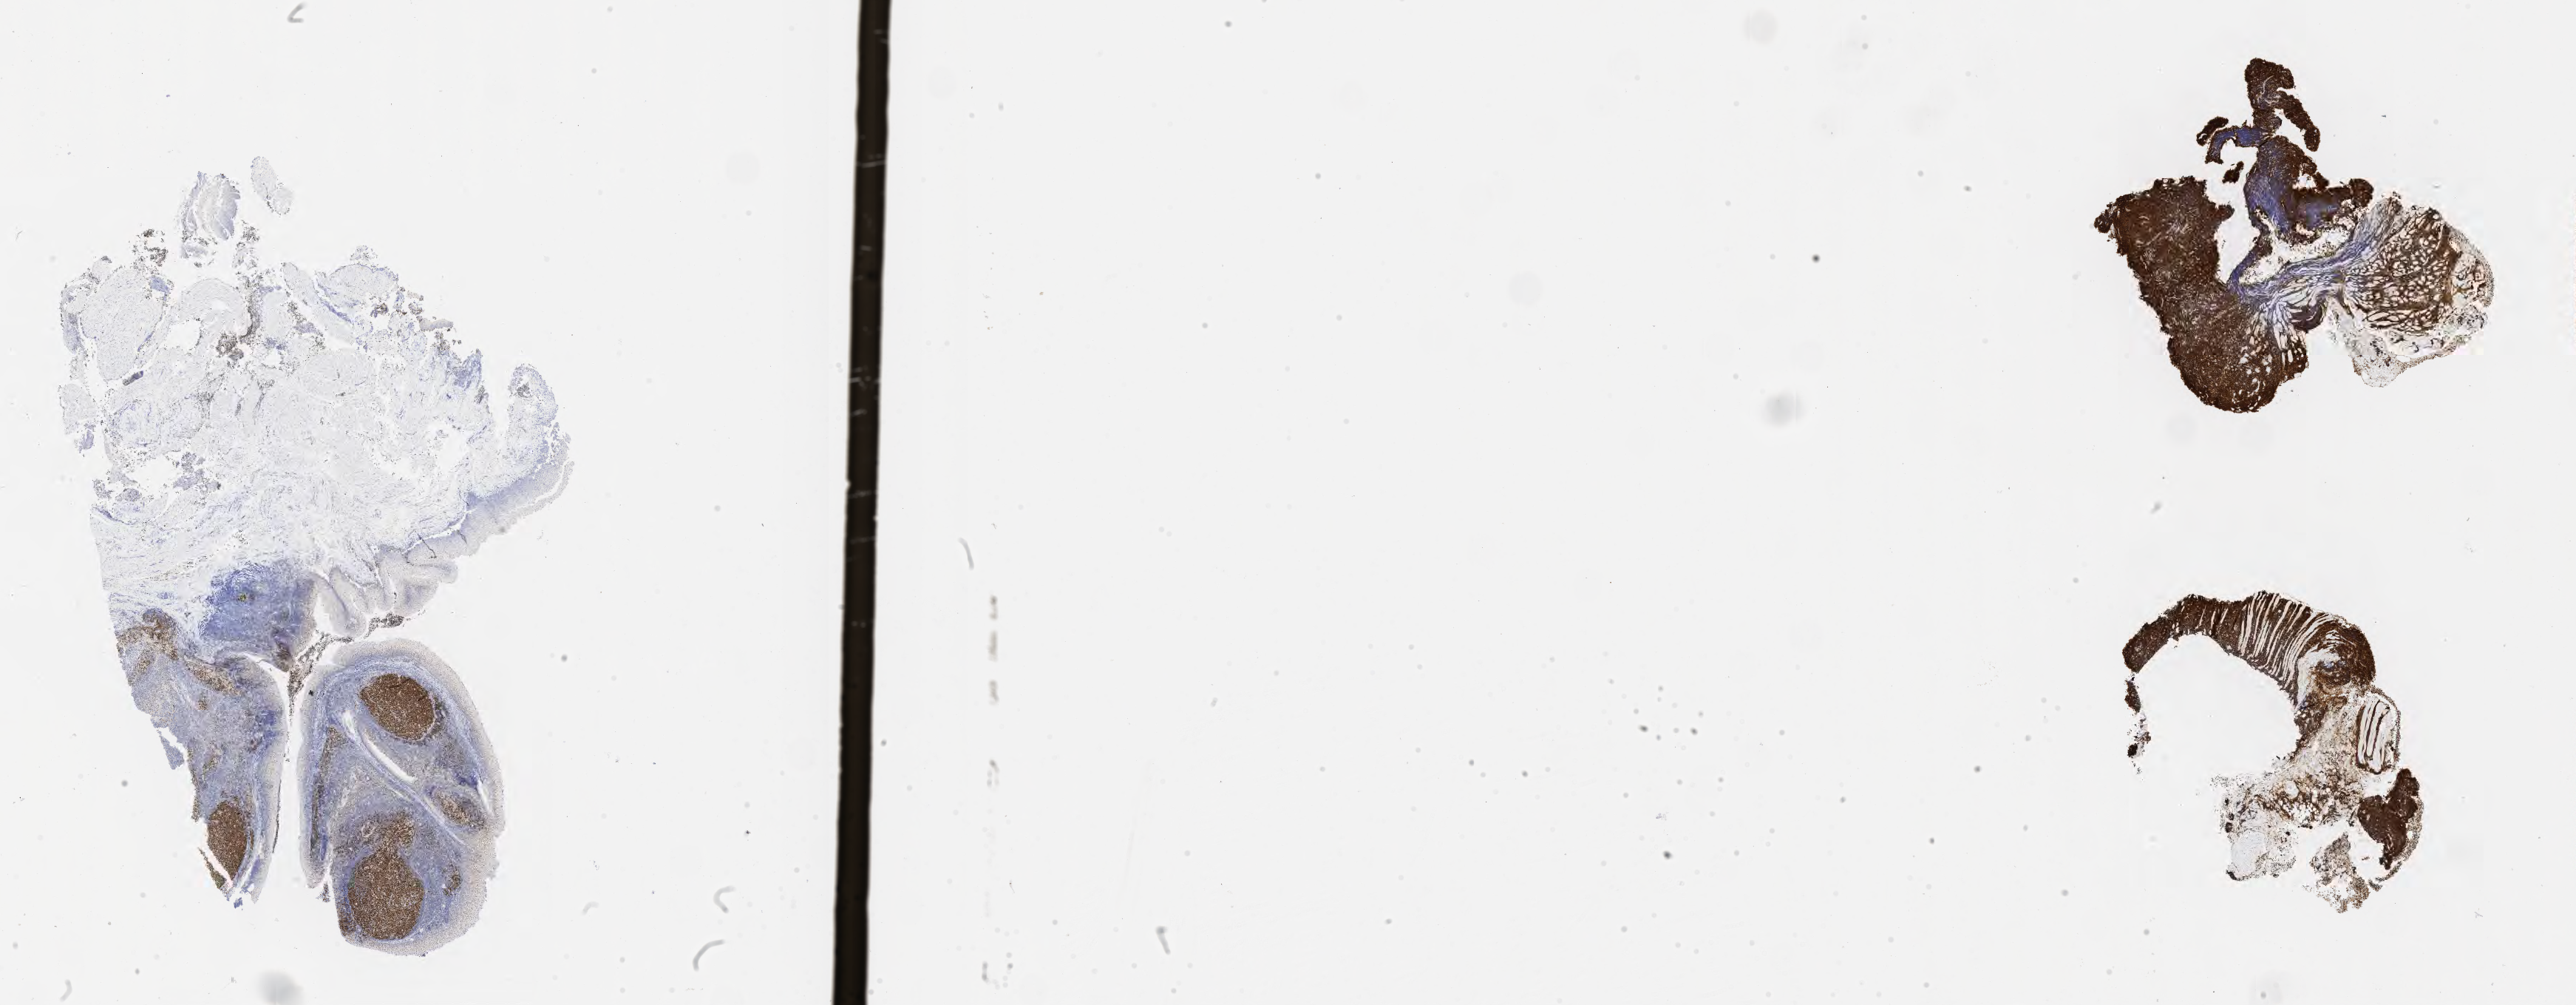
Whole-slide image, immunohistochemical stain for BCL6, shown as a low-resolution overview of the whole scanned area (about 28.2 x 11.0 mm). Tumor tissue. Anatomic site: lymph node of head and neck. Patient: male, age 73 years.
Diagnosis: Burkitt lymphoma, NOS.